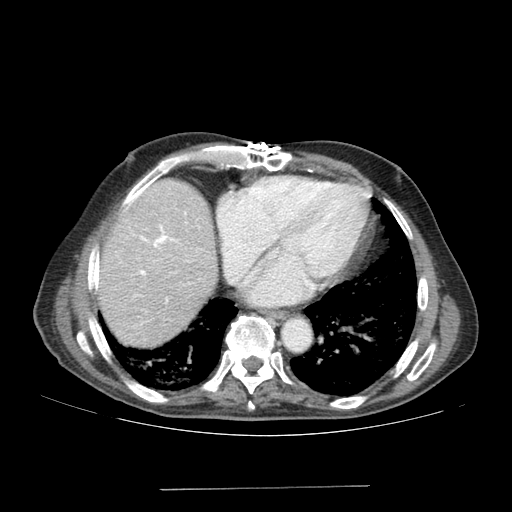
Contrast-enhanced abdominal CT (liver protocol), one axial slice; slice 158 of 192 in the series (ordered by position); soft-tissue window (W 400 / L 40 HU); 512 × 512 image matrix, field of view 400 × 400 mm. From the clinical record (not read from this slice): diagnosis: hepatocellular carcinoma (patient treated with transarterial chemoembolisation; whether this scan precedes or follows treatment is not stated here); TNM stage (as recorded): Stage-IVA.
Structures marked on this image (semi-automatic segmentation, software-assisted and operator-edited):
- liver parenchyma outside the tumour (the mass and vessels are separate outlines, so this box may not span the whole liver): bounding box [x1, y1, x2, y2] px = [96, 179, 216, 346]
- liver vessels: [128, 203, 186, 275]